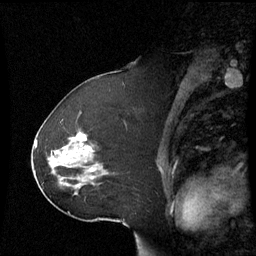
Breast MRI (dynamic contrast-enhanced), one sagittal slice. Position 38 of 60 along the scan axis. Dynamic contrast-enhanced series, image 2 of 3 at this slice position (ordered by acquisition). 1.5 T. TE 4.2 ms, TR 8.9 ms. 256 × 256 image matrix, field of view 230 × 230 mm. Female patient, age 51 years. From the clinical record (not read from this slice): setting: breast cancer imaged before/during neoadjuvant chemotherapy; receptor status: HR-positive, HER2-negative.
Outlined on this slice (semi-automatic segmentation, software-assisted and operator-edited):
- analysis volume of interest (the breast-tissue region the enhancement analysis was run in; not a lesion): bounding box <42,121,106,199> (left, top, right, bottom; pixels)
- tumour enhancement mask (voxels above the 70 % enhancement threshold inside the analysis volume of interest): <76,133,94,171>